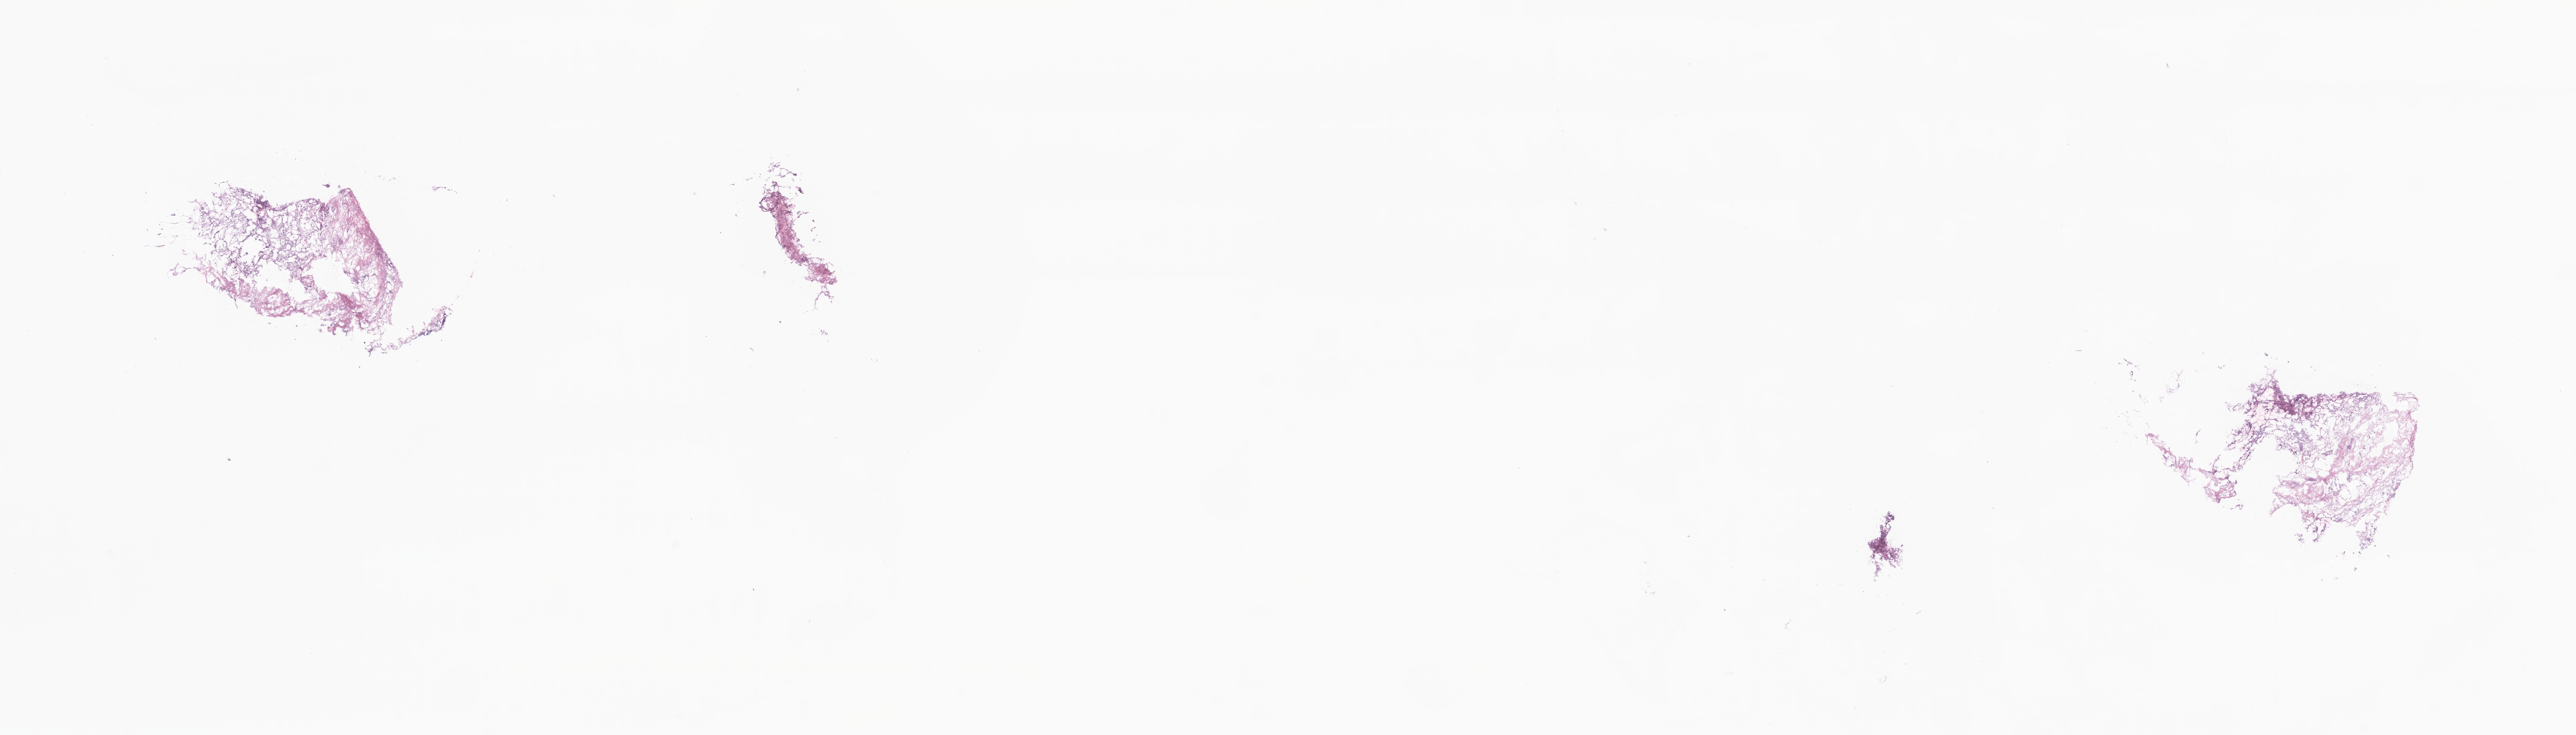
Haematoxylin and eosin whole-slide image, low-resolution overview of the scanned area, about 30.0 x 8.6 mm. Frozen section. Primary tumor. Anatomic site: breast (left). Female, age 73 years at initial diagnosis. Composition of this section per pathologist review: tumor cells 0%, tumor nuclei 0%, stromal cells 50%, necrosis 50%, normal cells 0%. Inflammatory infiltration, as recorded: lymphocyte infiltration 0%, monocyte infiltration 0%, neutrophil infiltration 0%.
Histologic diagnosis: Metaplastic carcinoma, NOS. Section: bottom of the tissue portion.